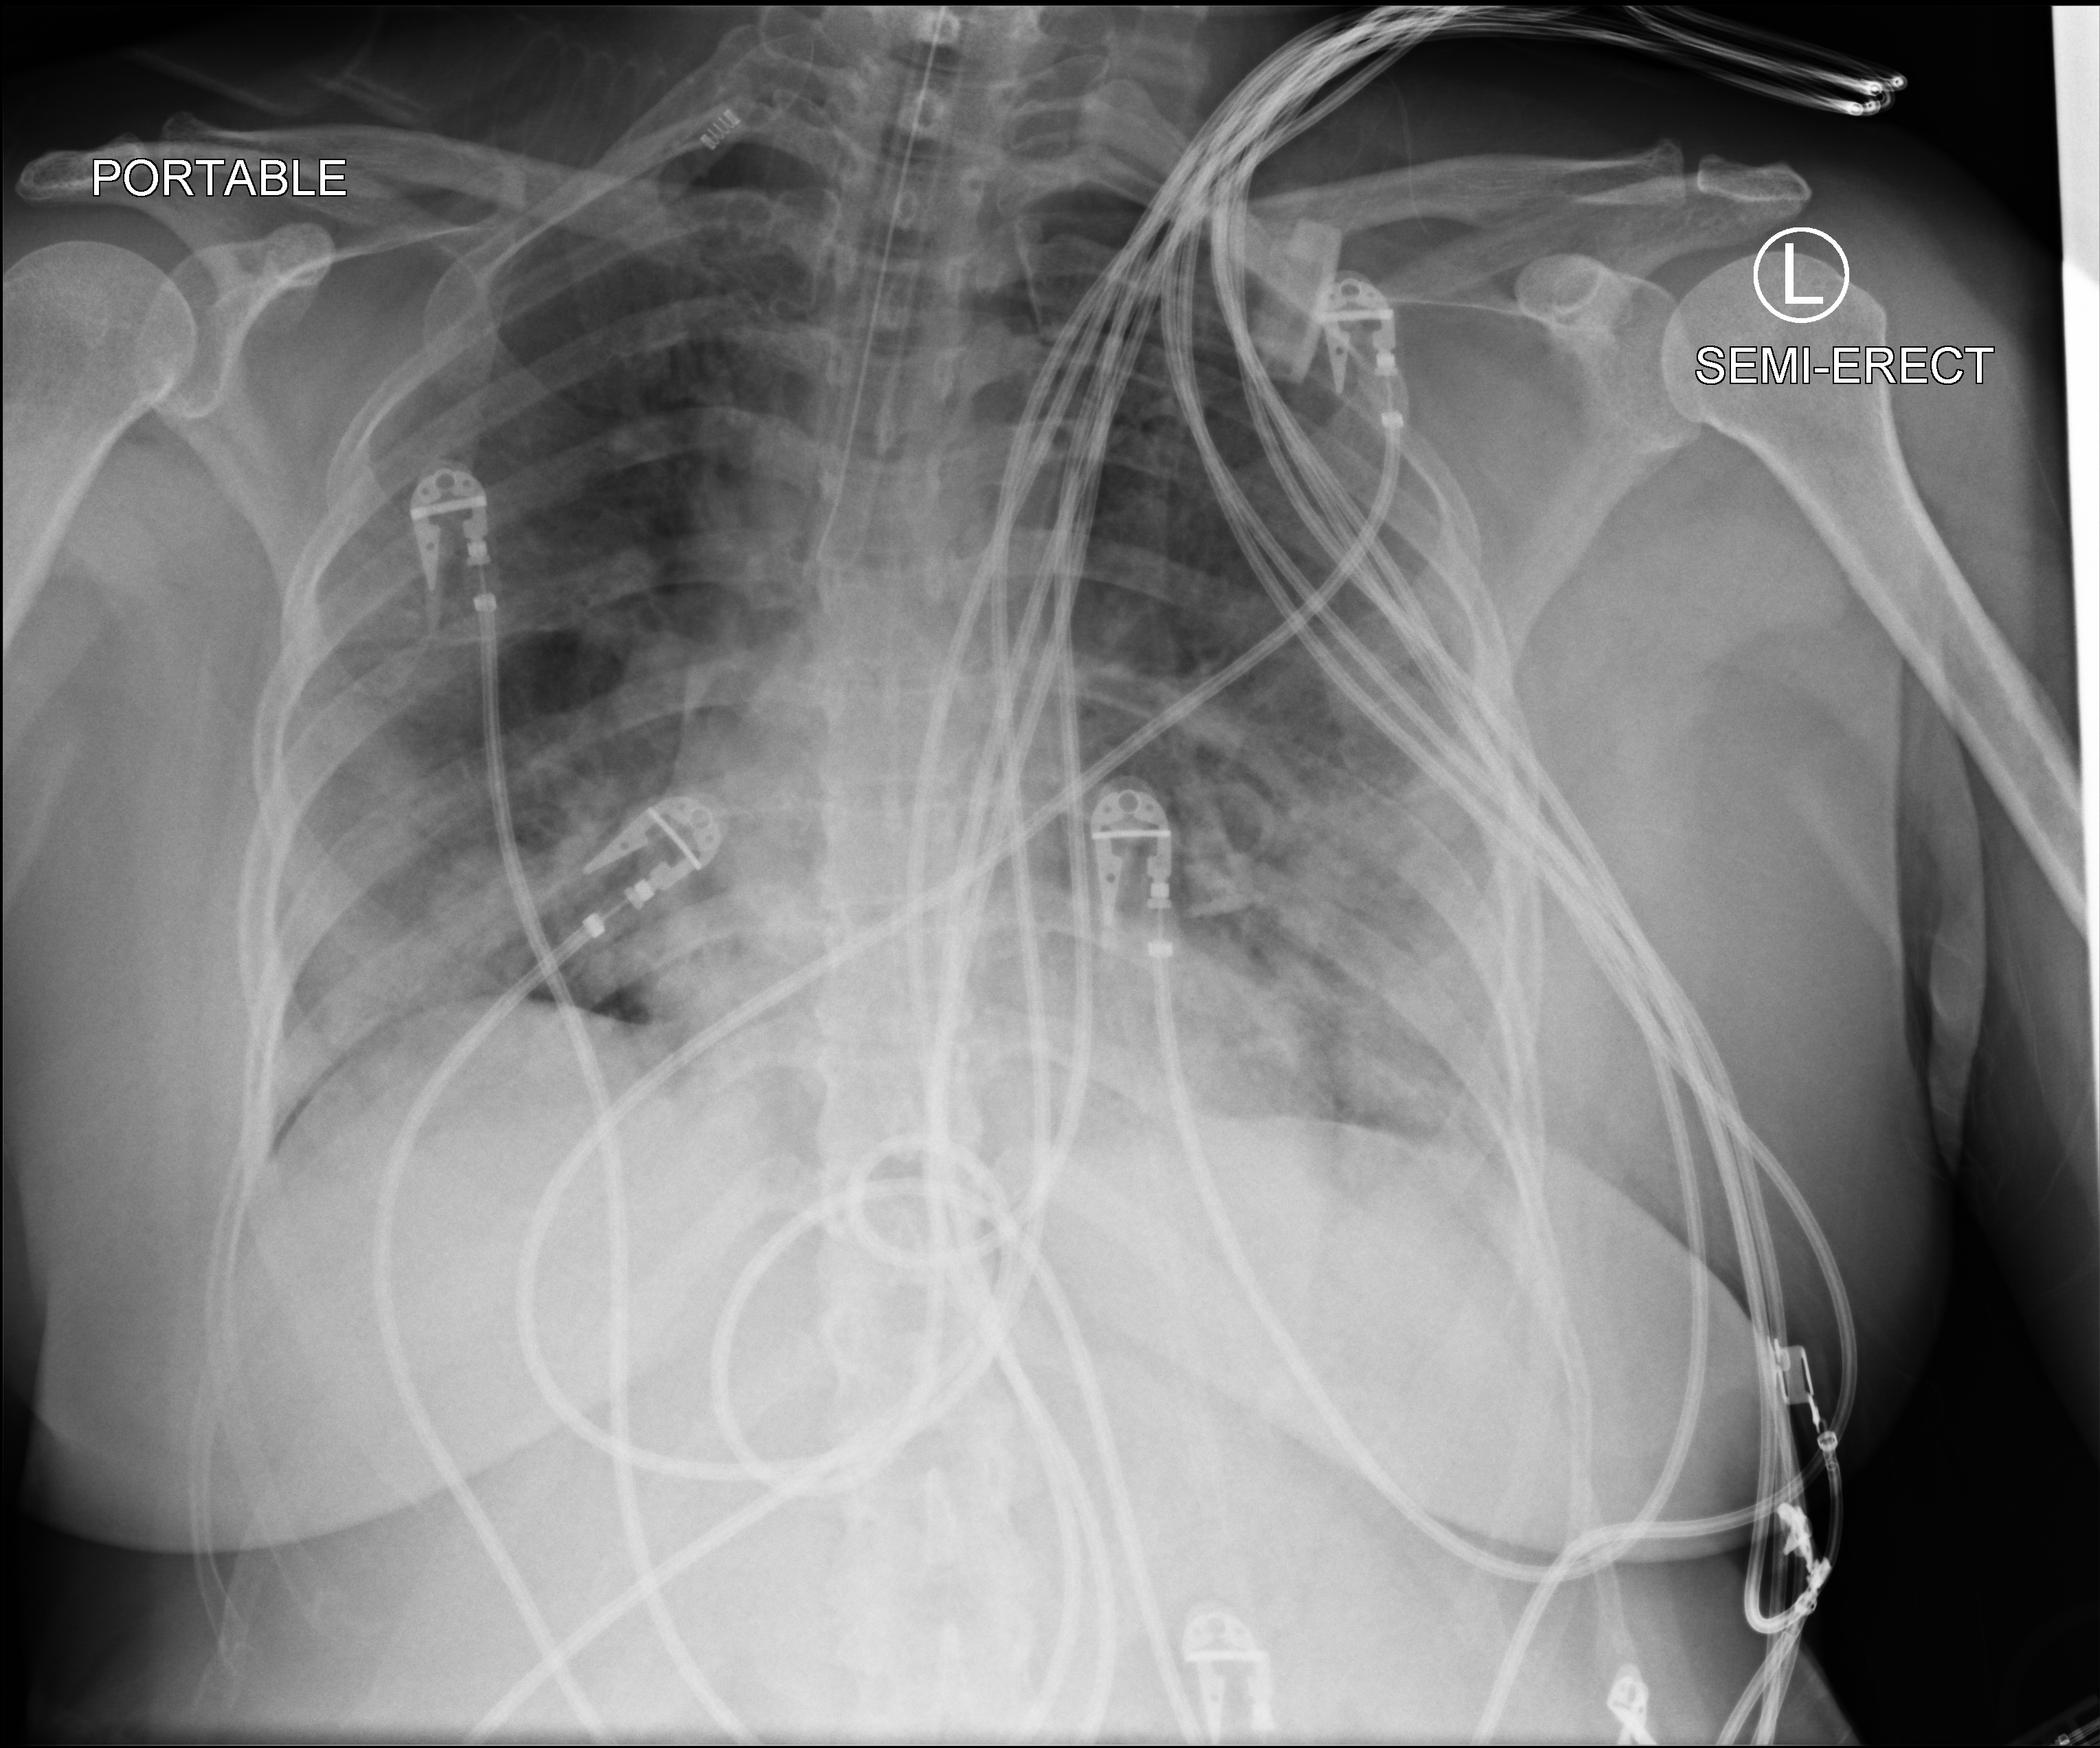
Bedside chest radiograph (computed radiography); anteroposterior (AP) projection. Male patient hospitalised with COVID-19, age 18–59 years.
Admission-level facts for this patient (not findings on this image; timing relative to this image not recorded): admitted to intensive care during this hospital stay: yes; mechanically ventilated during this hospital stay: yes.